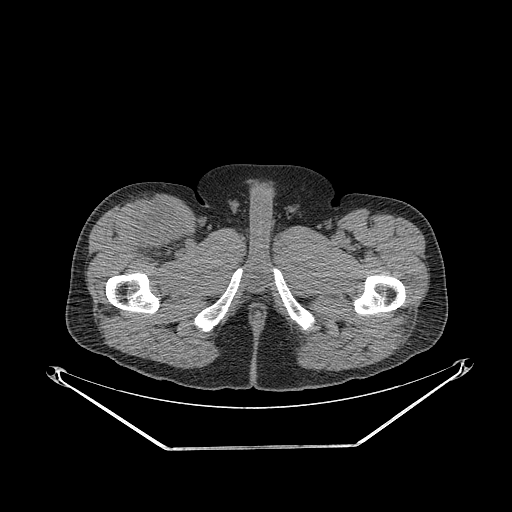
CT of an extremity soft-tissue mass (from a PET/CT study), one axial slice. Position 303 of 311 along the scan axis. 140 kVp. Soft-tissue window (W 400 / L 40 HU). 3.75 mm slice thickness. 512 × 512 image matrix. Male patient. From the clinical record (not read from this slice): histological type: pleiomorphic leiomyosarcoma; grade: intermediate; site of the primary tumour: right thigh.
Annotated regions visible in this slice (expert contour drawn on MRI and transferred to this co-registered scan by the dataset authors):
- gross tumour volume including surrounding oedema: bounding box (x1, y1, x2, y2) in pixels: (130, 199, 184, 250)
- gross tumour volume (mass): (137, 208, 181, 248)